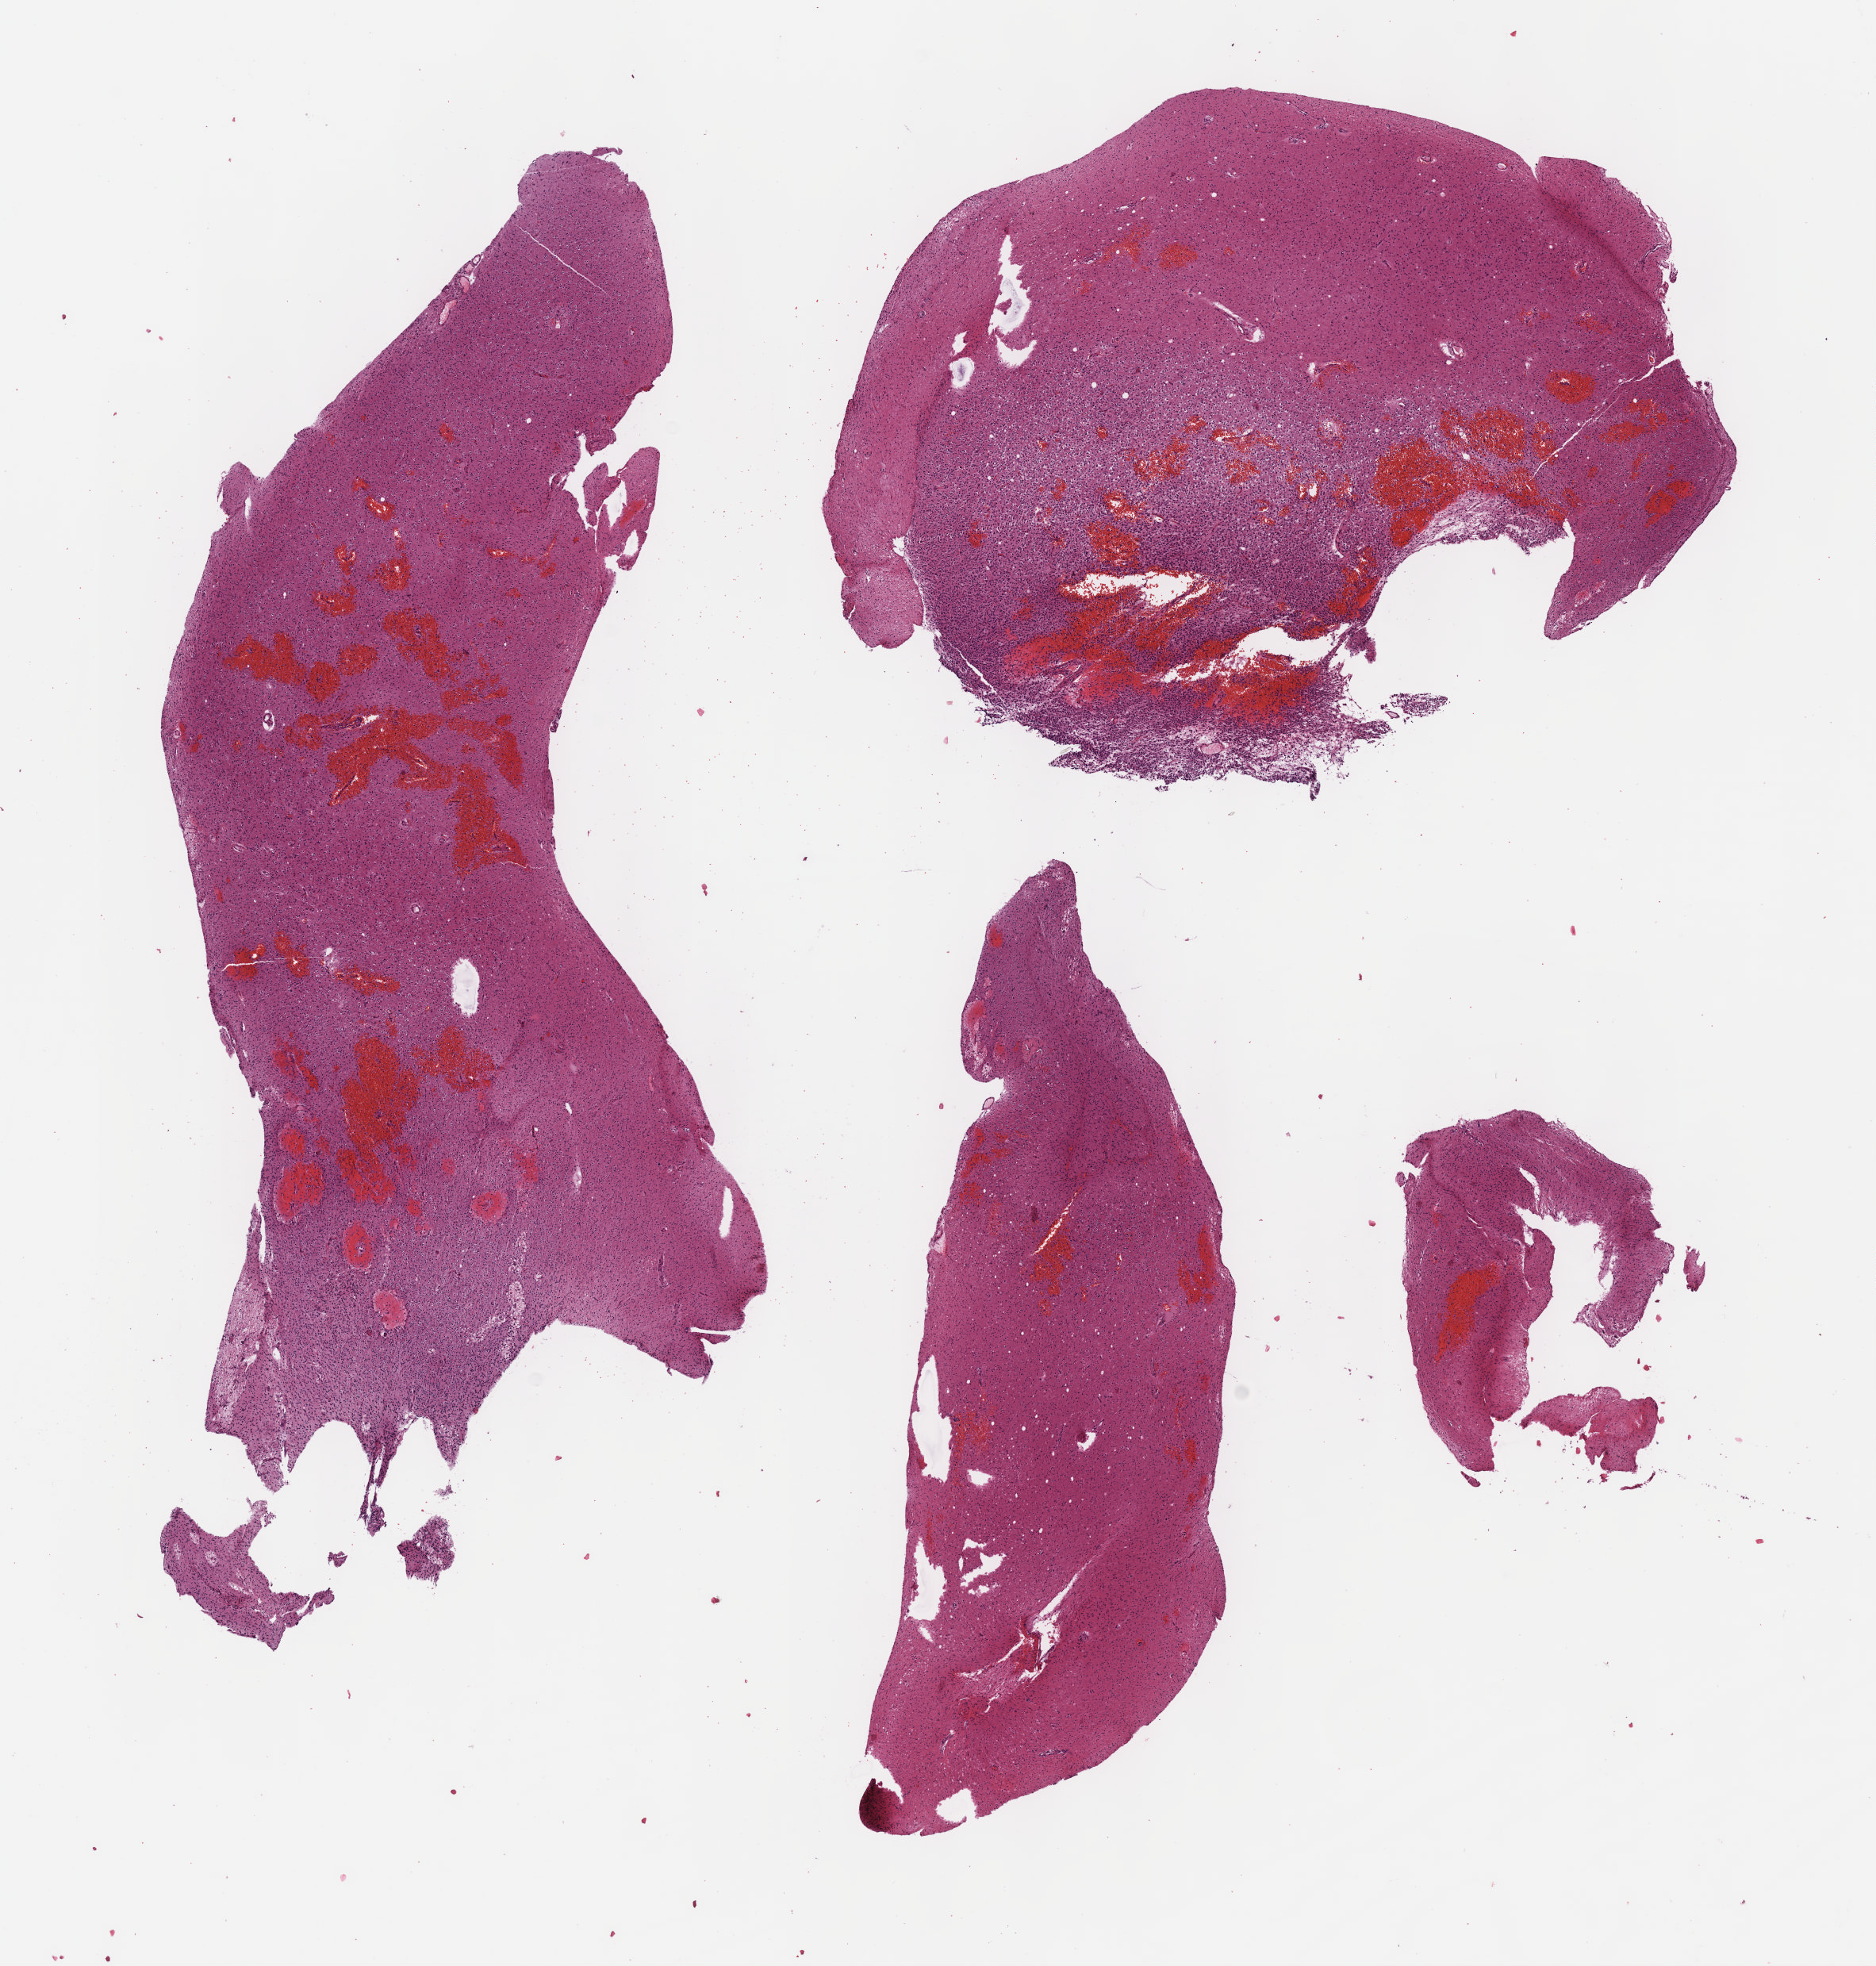
H&E whole-slide image — shown as a low-resolution overview of the whole scanned area (about 9.6 x 10.0 mm, acquisition: 40x scan). Formalin-fixed paraffin-embedded (FFPE) diagnostic section. Brain, primary tumour sample. Male, age 53 years at initial diagnosis. Histologic grade: G3 (poorly differentiated).
* histologic diagnosis: Oligodendroglioma, anaplastic
* laterality: left